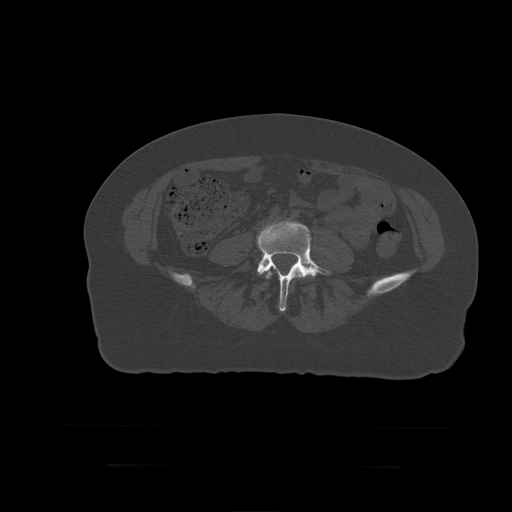
CT including the spine, one axial slice. Position 79 of 399 along the scan axis. Reconstruction kernel STANDARD. 120 kVp. Bone window (W 1800 / L 400 HU). 1.25 mm slice thickness. 512 × 512 image matrix, field of view 450 × 450 mm. Patient age 41 years. From the clinical record (not read from this slice): primary cancer: breast.
Outlined on this slice (semi-automatically segmented with operator editing):
- L4 vertebra: bounding box <266,263,297,279> (left, top, right, bottom; pixels)
- L5 vertebra: <257,221,331,312>